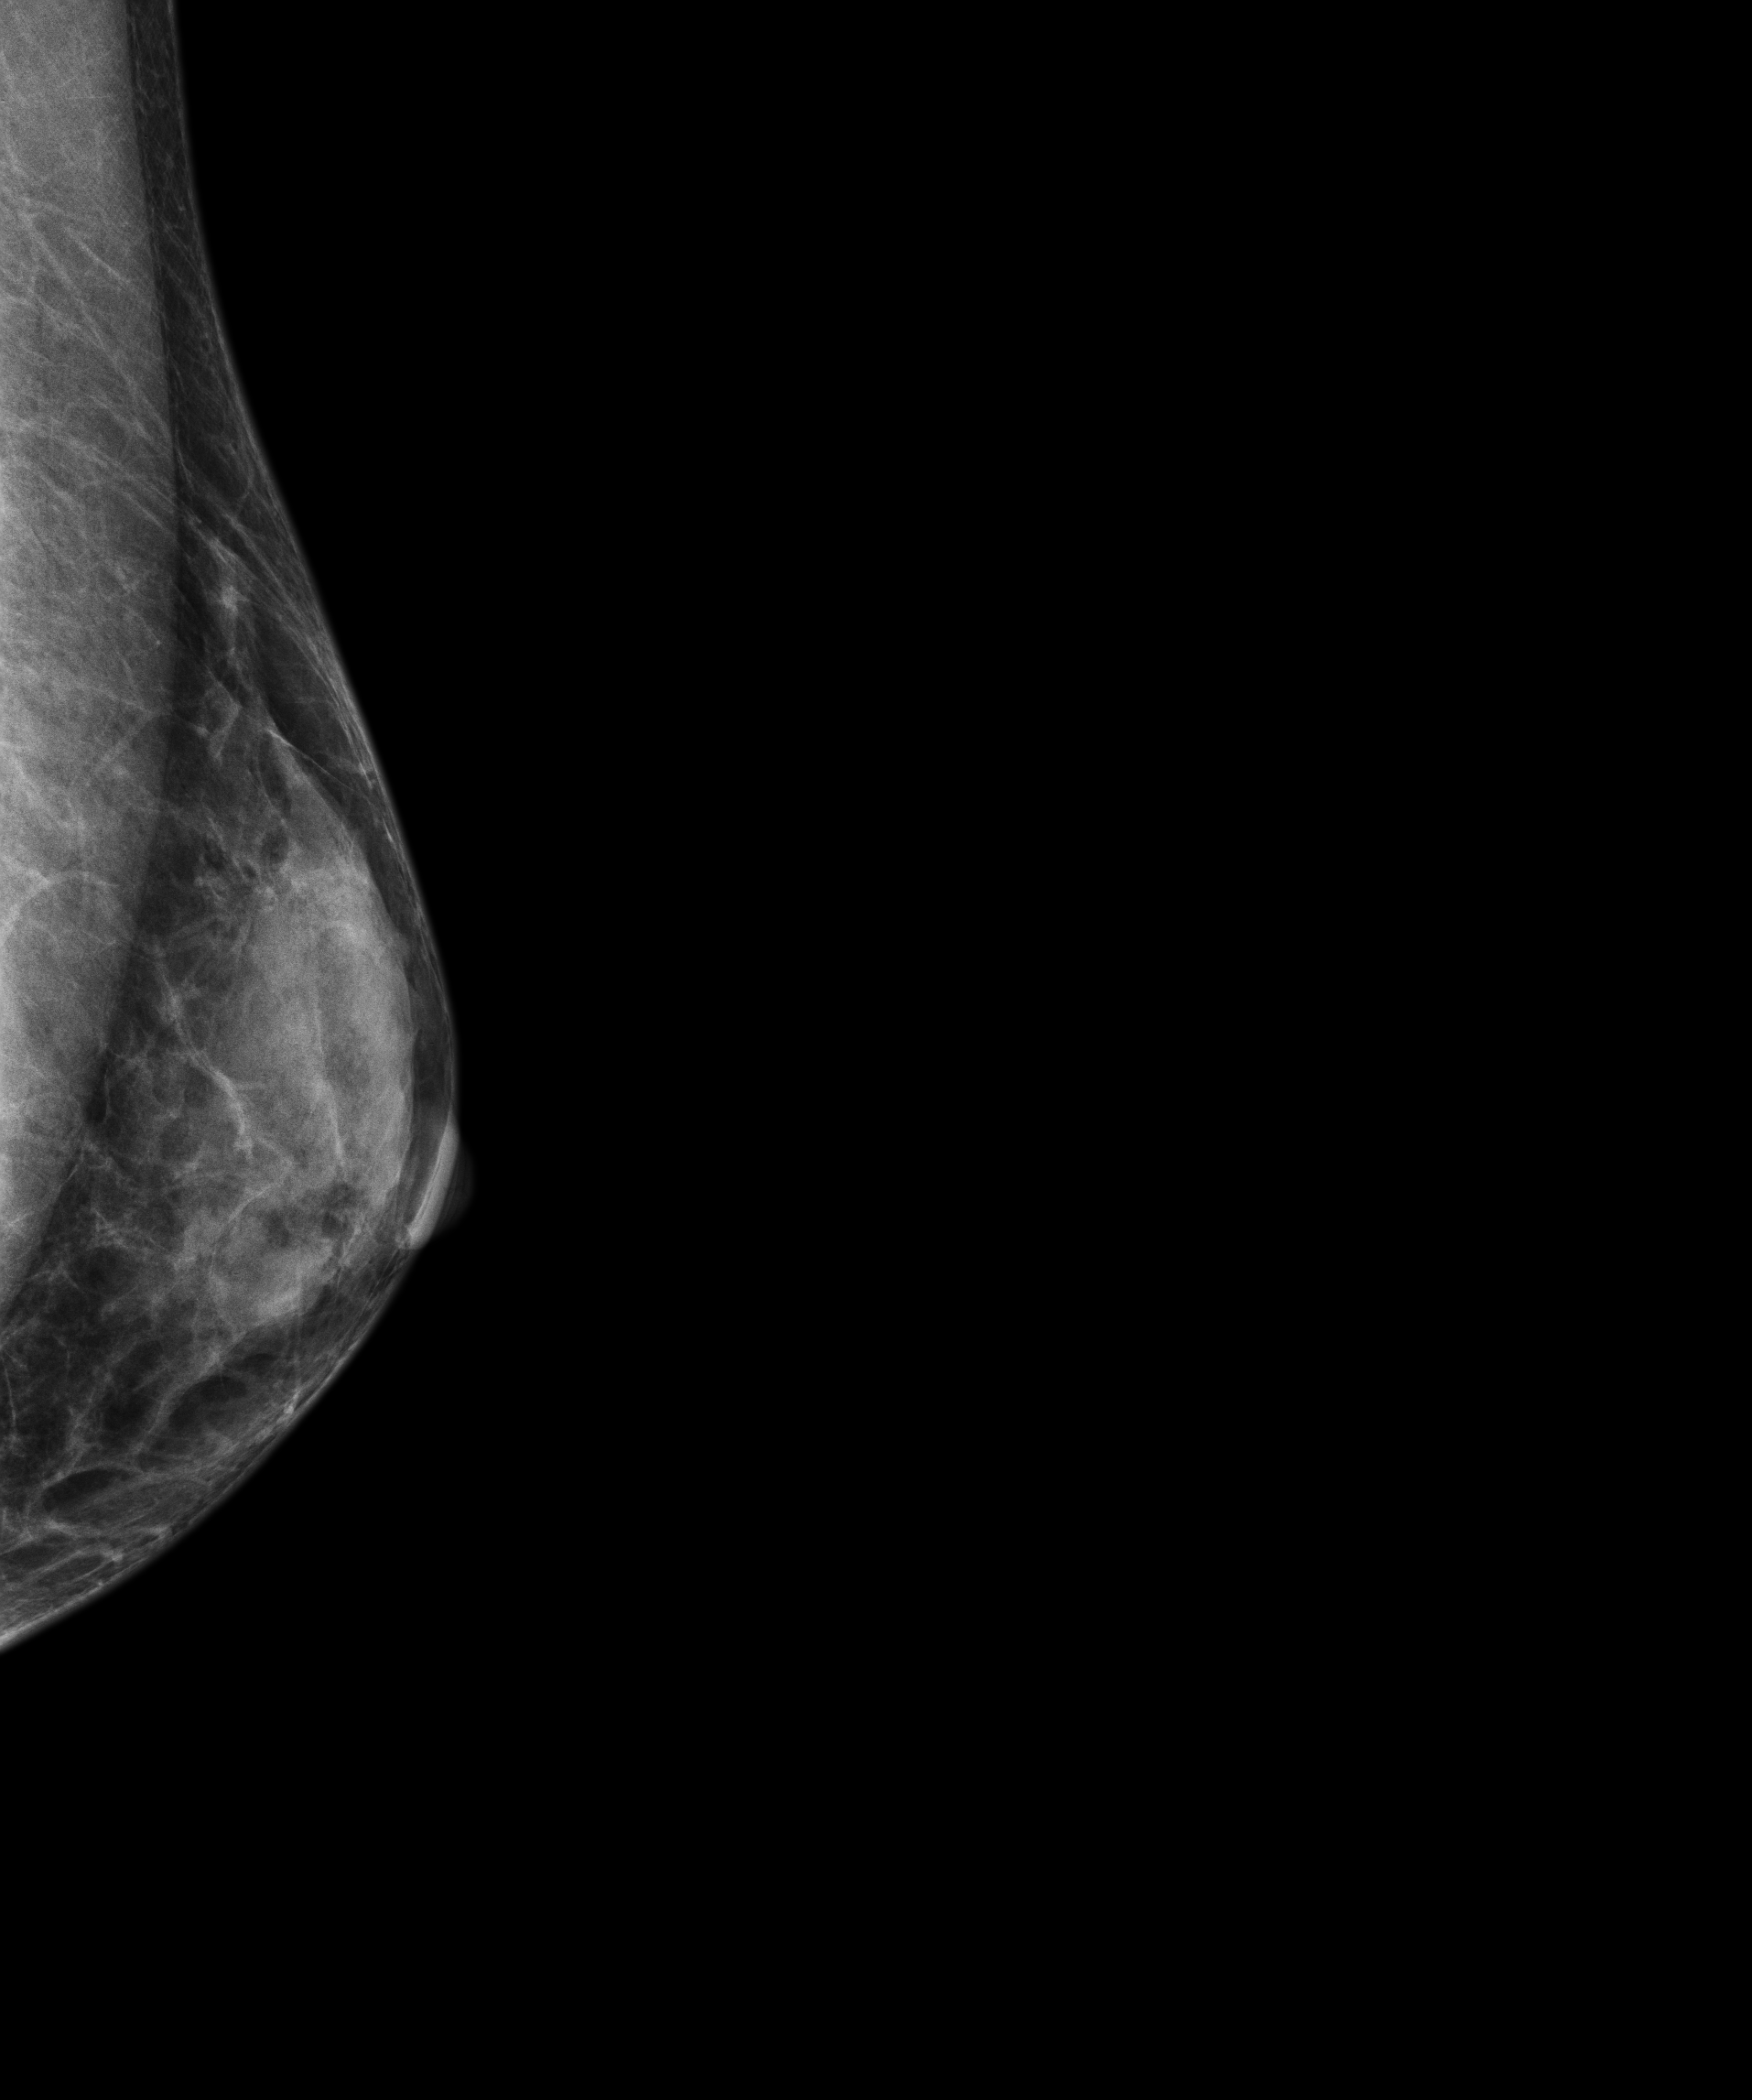
Screening examination; compressed breast thickness 29 mm. Female patient, age 55 years.
Image type: full-field digital mammogram. Breast: left. Projection: exaggerated CC view (lateral).